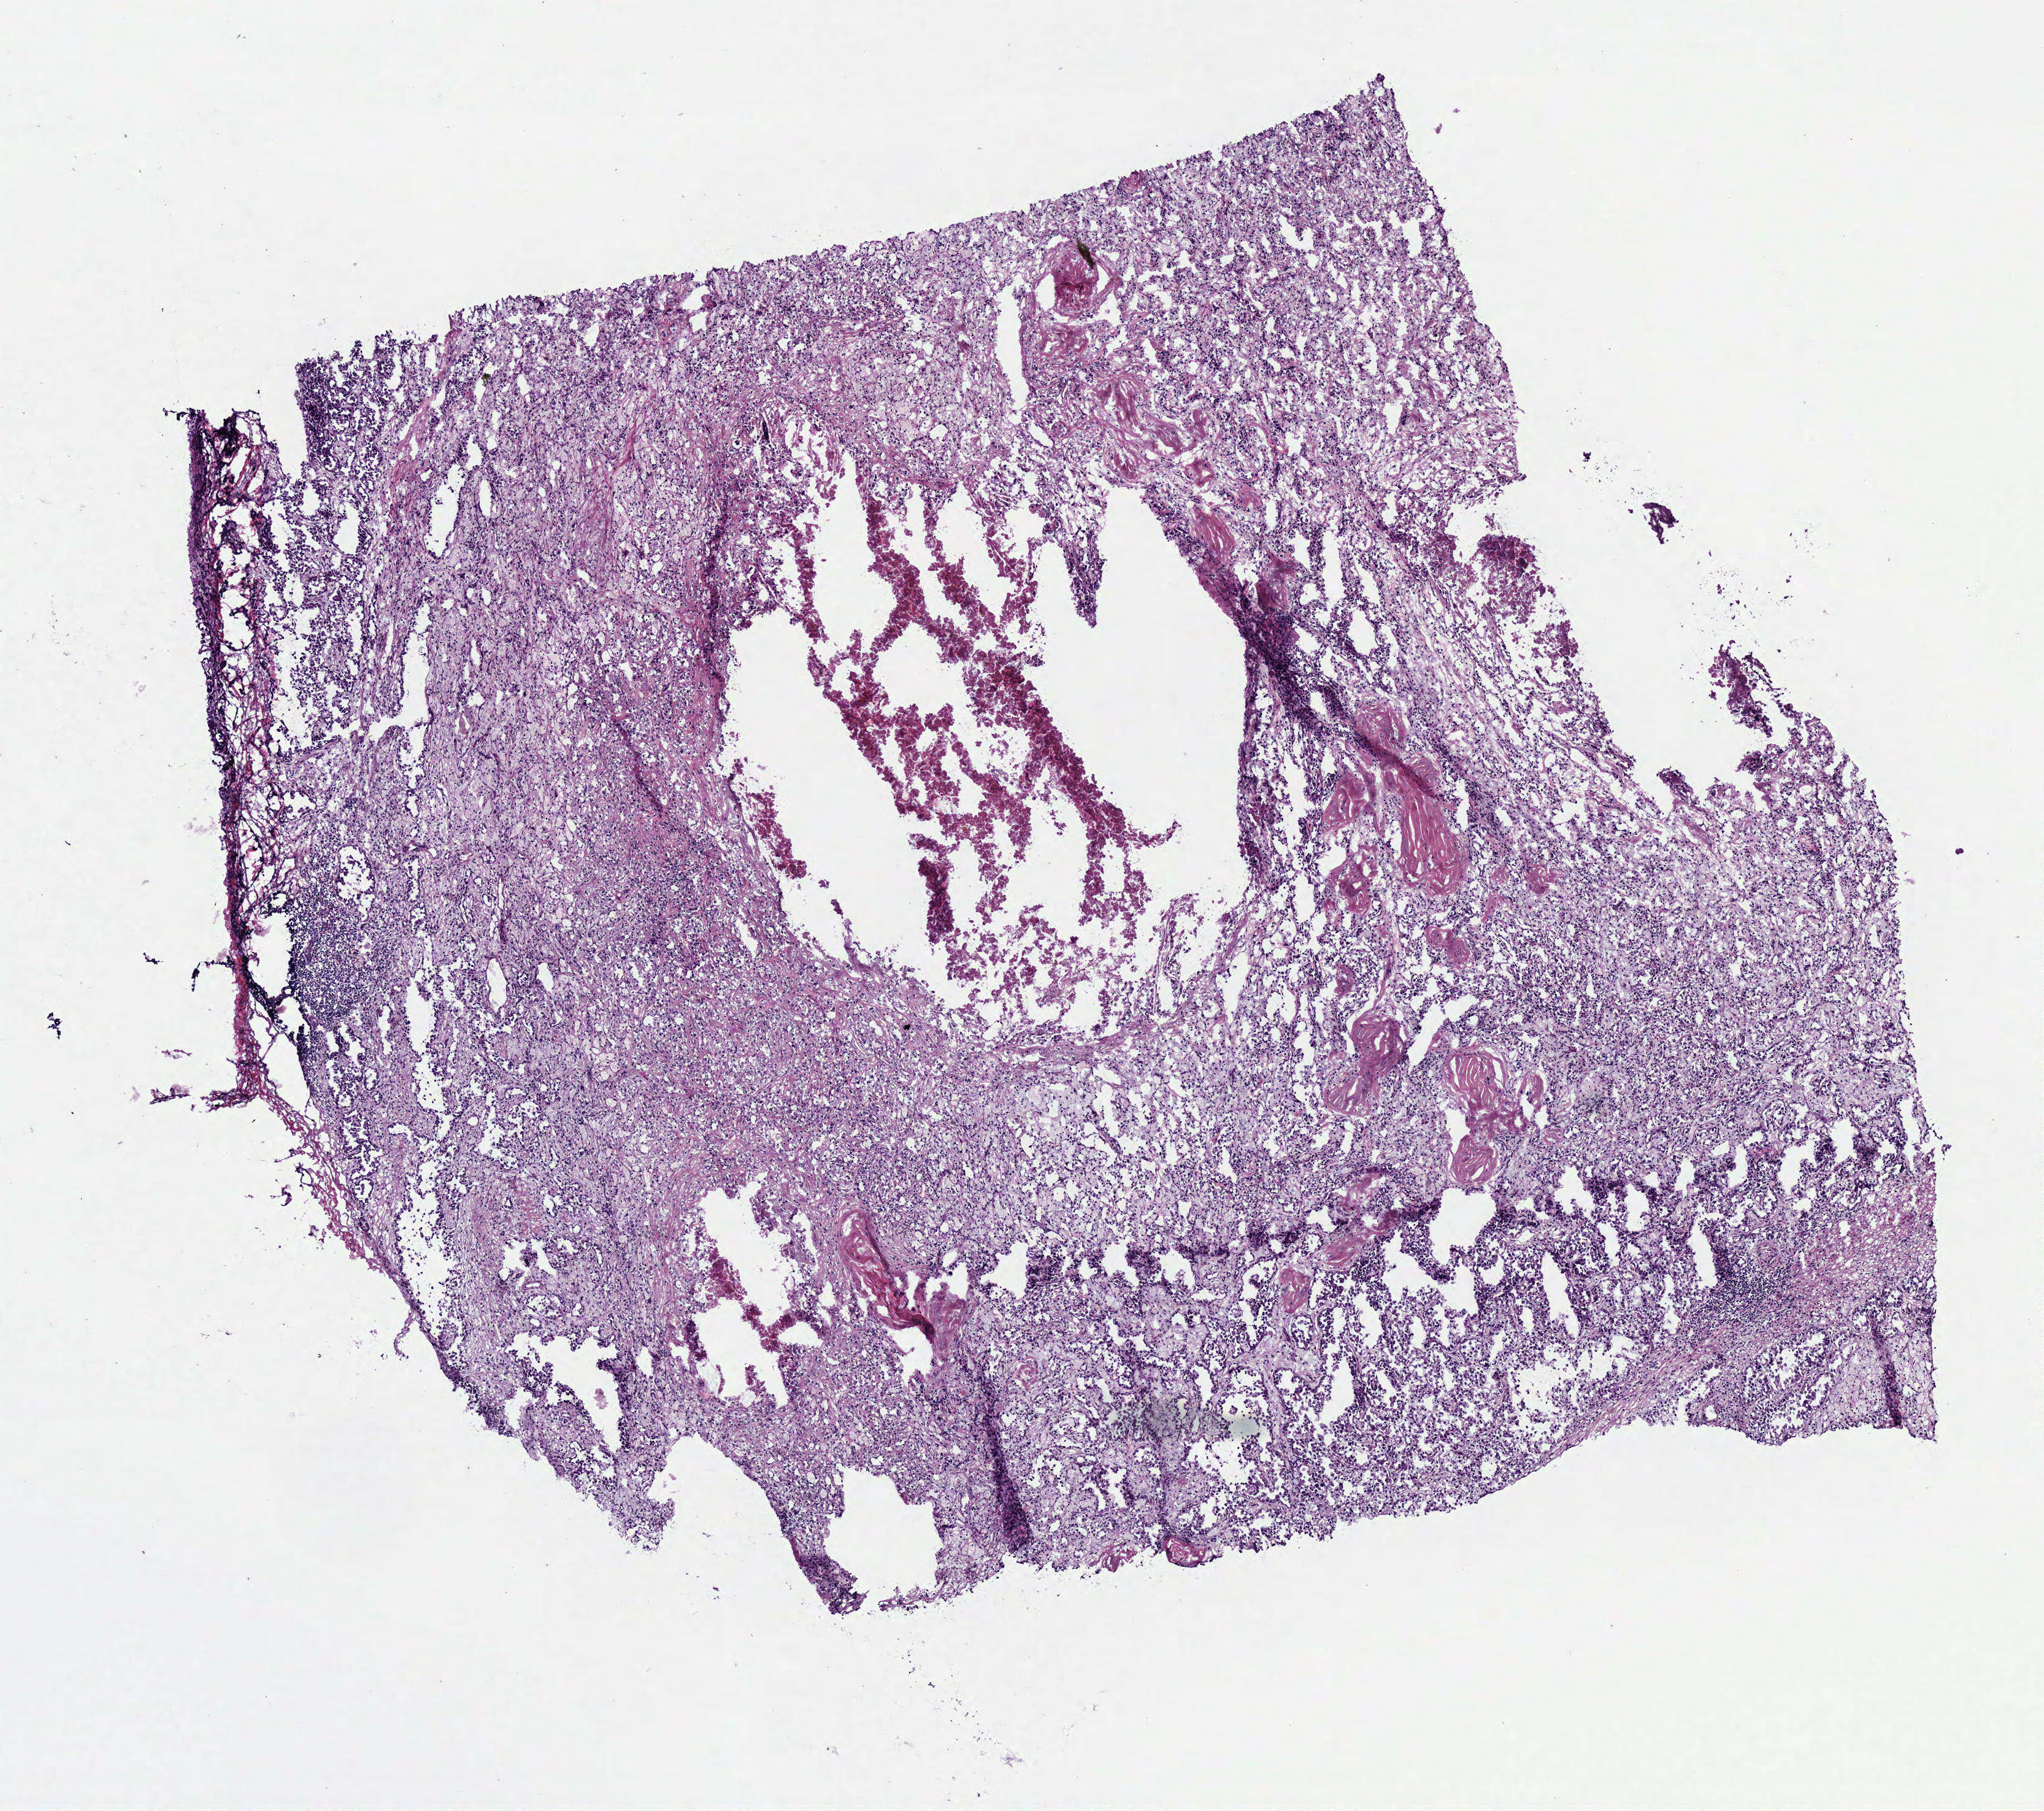
Digitized Hematoxylin and eosin (H&E) stained tissue section (whole slide) — whole scanned area (about 6.6 x 5.8 mm) shown as a low-resolution overview. Frozen section from the bottom of the tissue portion. Sample: primary tumour, kidney. Male, age 69 years at initial diagnosis. Pathologist review of this section (percent, as recorded): tumour cells 70%, tumour nuclei 75%, normal cells 0%, stromal cells 15%, necrosis 15%.
Pathologic diagnosis: Papillary adenocarcinoma, NOS. AJCC pathologic stage: I (6th edition).